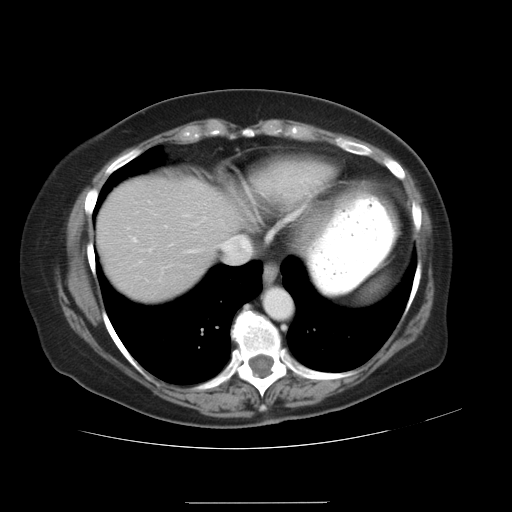
Contrast-enhanced abdominal CT, one axial slice; position 27 of 32 along the scan axis; reconstruction kernel STANDARD; 120 kVp; intravenous contrast given; soft-tissue window (W 400 / L 40 HU); 512 × 512 image matrix, field of view 386 × 386 mm. Female patient, age 65 years. Case-level facts recorded for this patient, not image findings: diagnosis: colorectal cancer liver metastases, imaged before liver resection; multiple liver metastases: yes.
Structures marked on this image (manually delineated by an expert):
- hepatic veins: box from (x=182, y=224) to (x=252, y=263) px
- liver: (x=98, y=173)–(x=303, y=302)
- planned liver remnant (the part of the liver to remain after resection): (x=98, y=178)–(x=237, y=302)